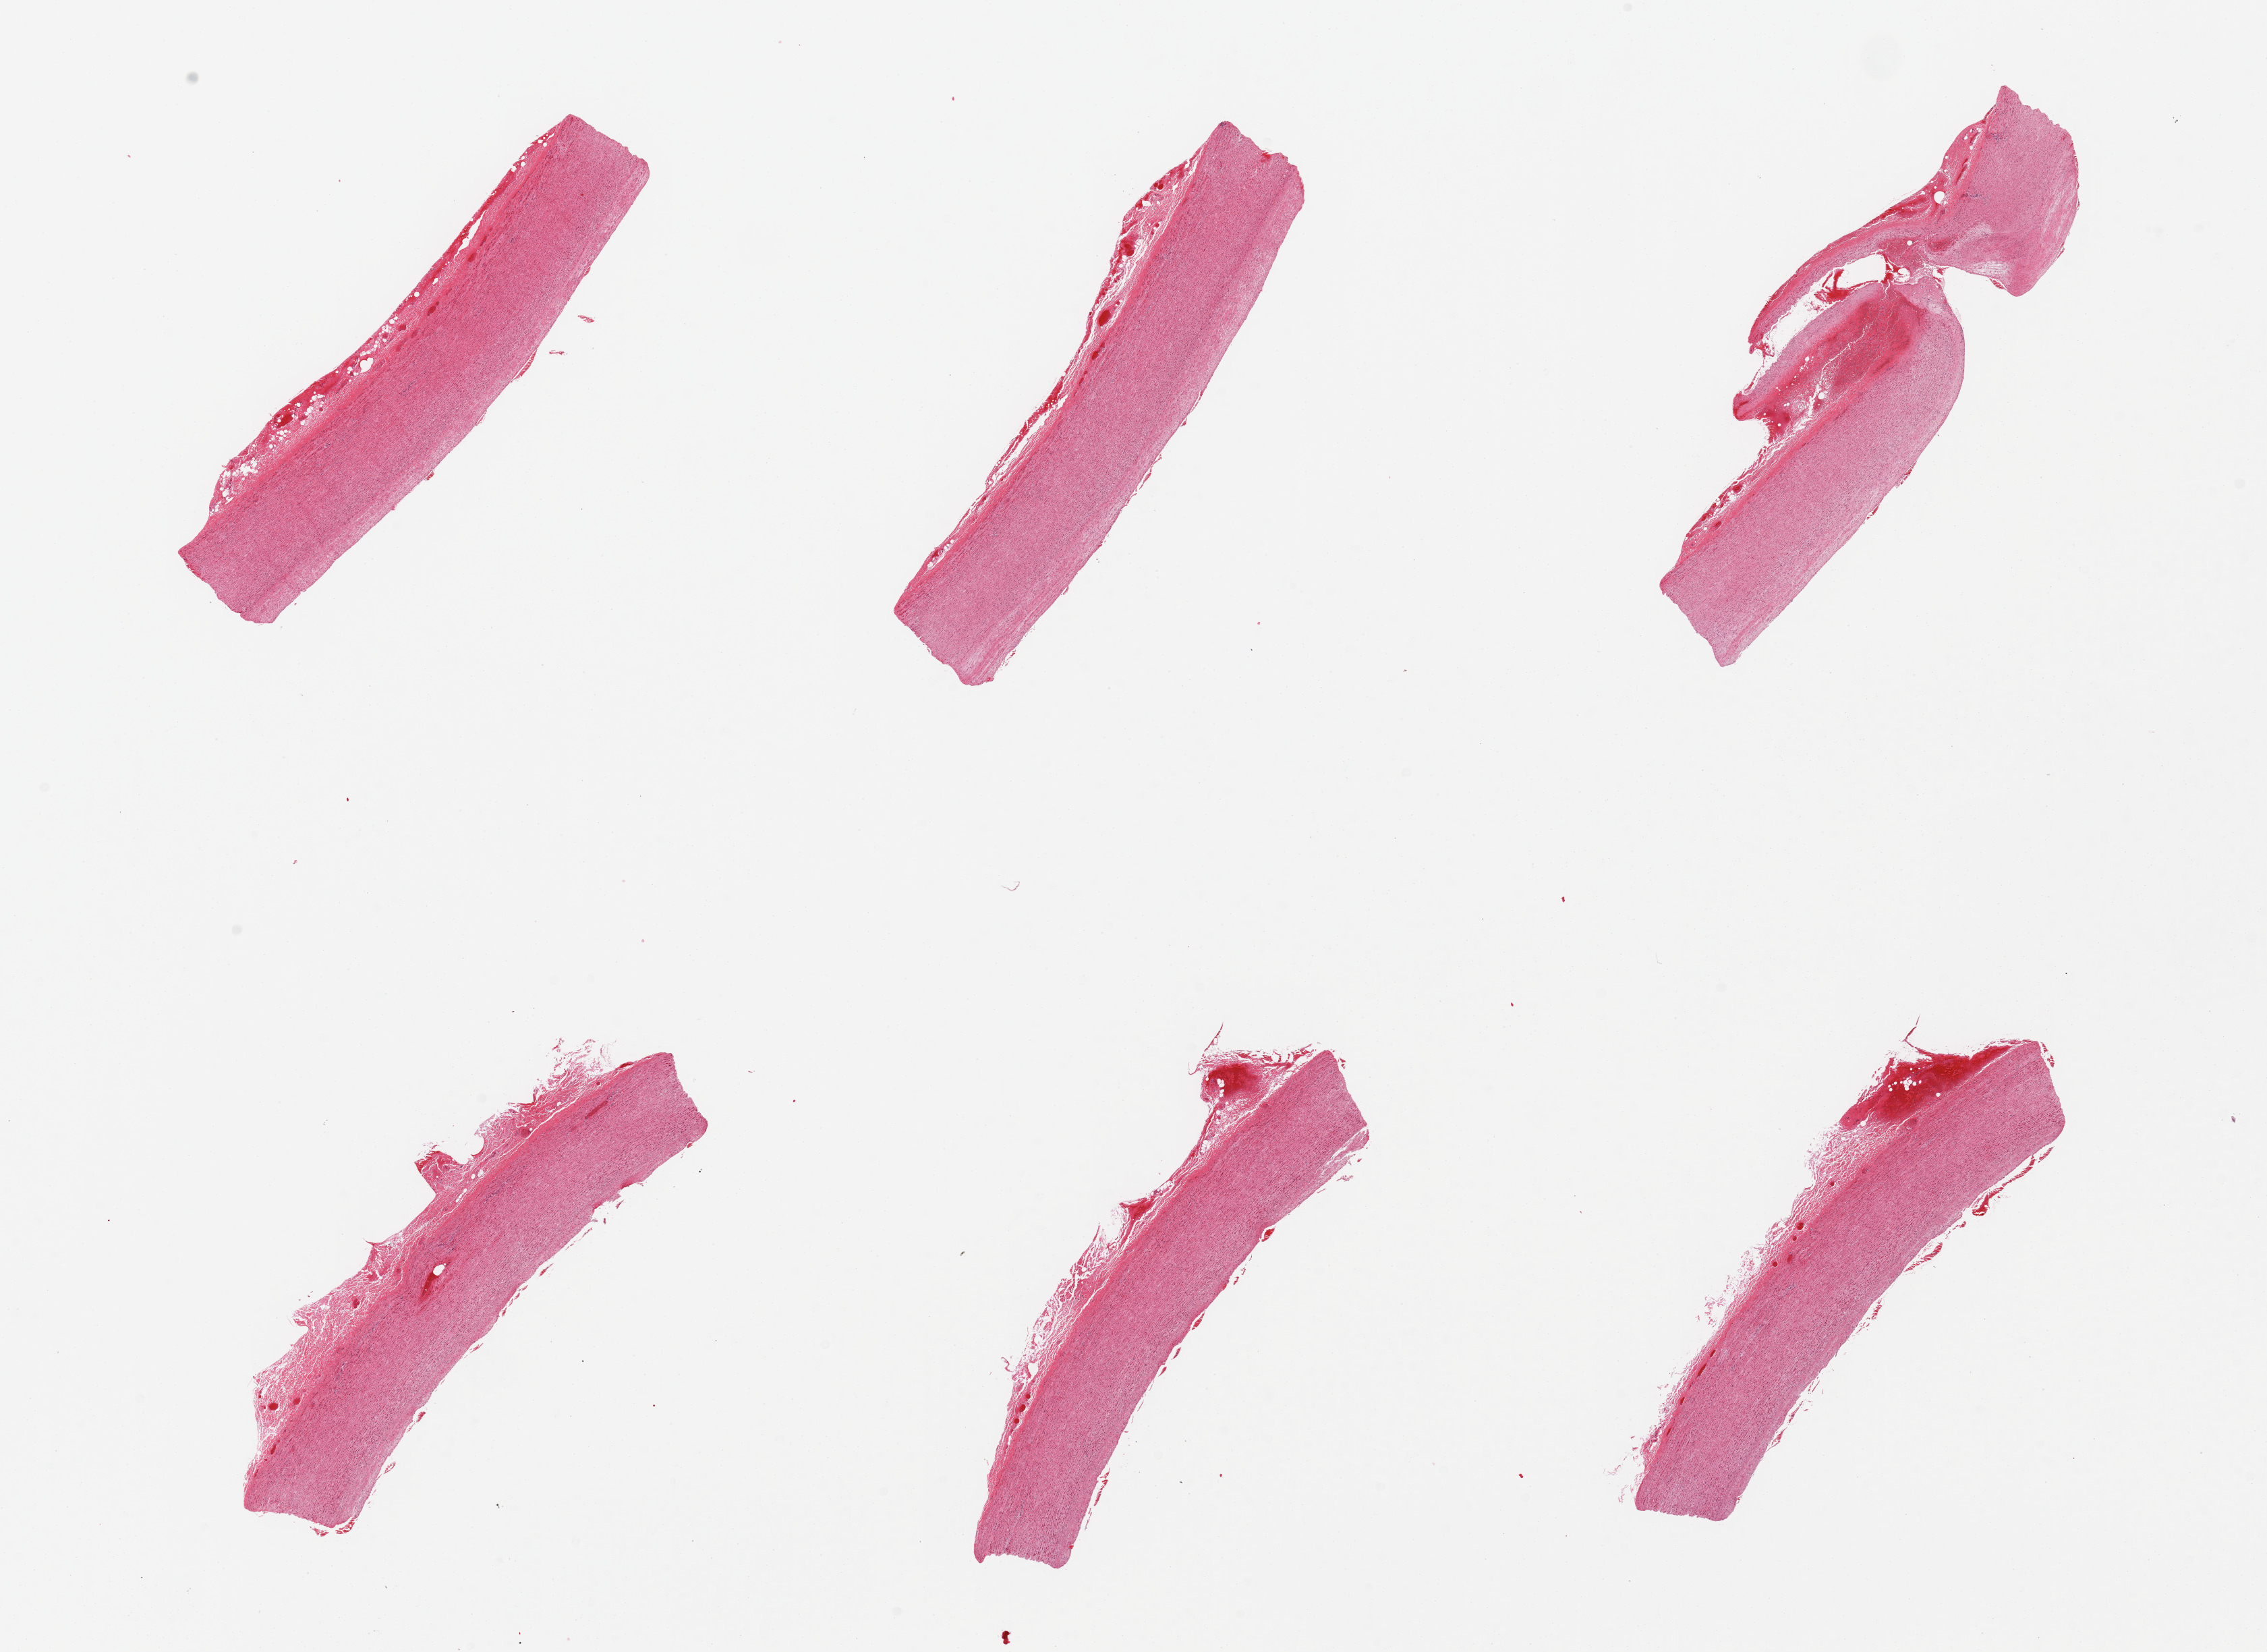
Whole-slide image, hematoxylin and eosin (H&E) stain, a low-resolution overview of the entire scanned area, about 26.6 x 19.4 mm (from a 20x scan); PAXgene-fixed paraffin-embedded (PFPE) section; sampled site (target tissue): aorta; tissue donor sample.
Review note (as recorded): 6 piece, adherent vas vasorum, ~0.5mm.